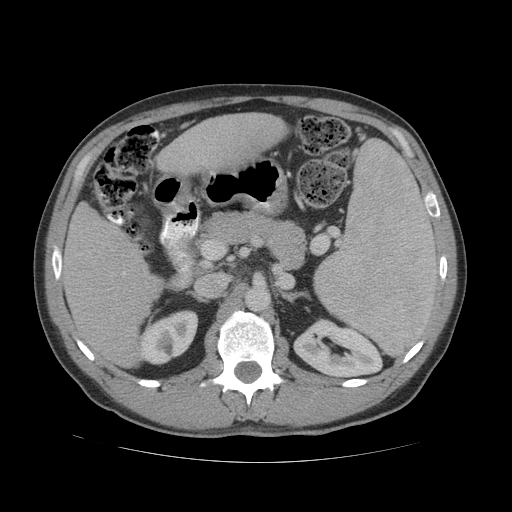
Contrast-enhanced abdominal CT (liver protocol), one axial slice. Slice 27 of 81 in the series (ordered by position). 140 kVp. Soft-tissue window (W 400 / L 40 HU). 512 × 512 image matrix, field of view 400 × 400 mm. Case-level facts recorded for this patient, not image findings: diagnosis: hepatocellular carcinoma (patient treated with transarterial chemoembolisation; whether this scan precedes or follows treatment is not stated here); TNM stage (as recorded): Stage-IVB; Child-Pugh class: B; tumour differentiation: well differentiated; tumour nodularity: multinodular.
Structures marked on this image (semi-automatically segmented with operator editing):
- liver parenchyma outside the tumour (the mass and vessels are separate outlines, so this box may not span the whole liver): bounding box [x1, y1, x2, y2] px = [60, 112, 286, 366]
- liver vessels: [123, 272, 126, 275]